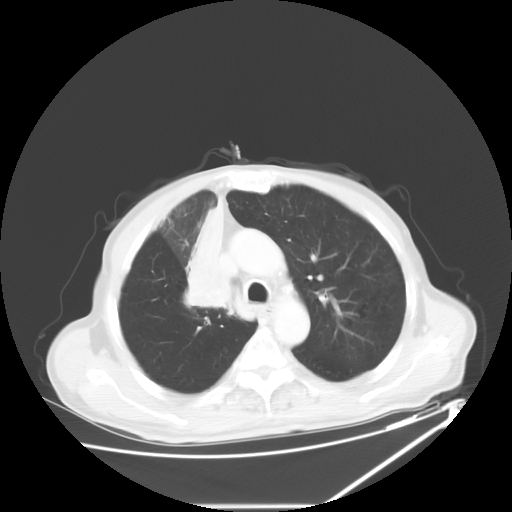
Chest CT, one axial slice. Position 44 of 60 along the scan axis. Lung window (W 1500 / L -600 HU). 5 mm slice thickness. 512 × 512 image matrix, field of view 410 × 410 mm. Male patient, age 73 years. From the clinical record (not read from this slice): clinical TNM (as recorded): T2a N1 M0.
Structures marked on this image (rectangle marked by the reading radiologist):
- lung tumour (recorded histology: squamous cell carcinoma): bounding box (x1, y1, x2, y2) in pixels: (175, 194, 235, 325)